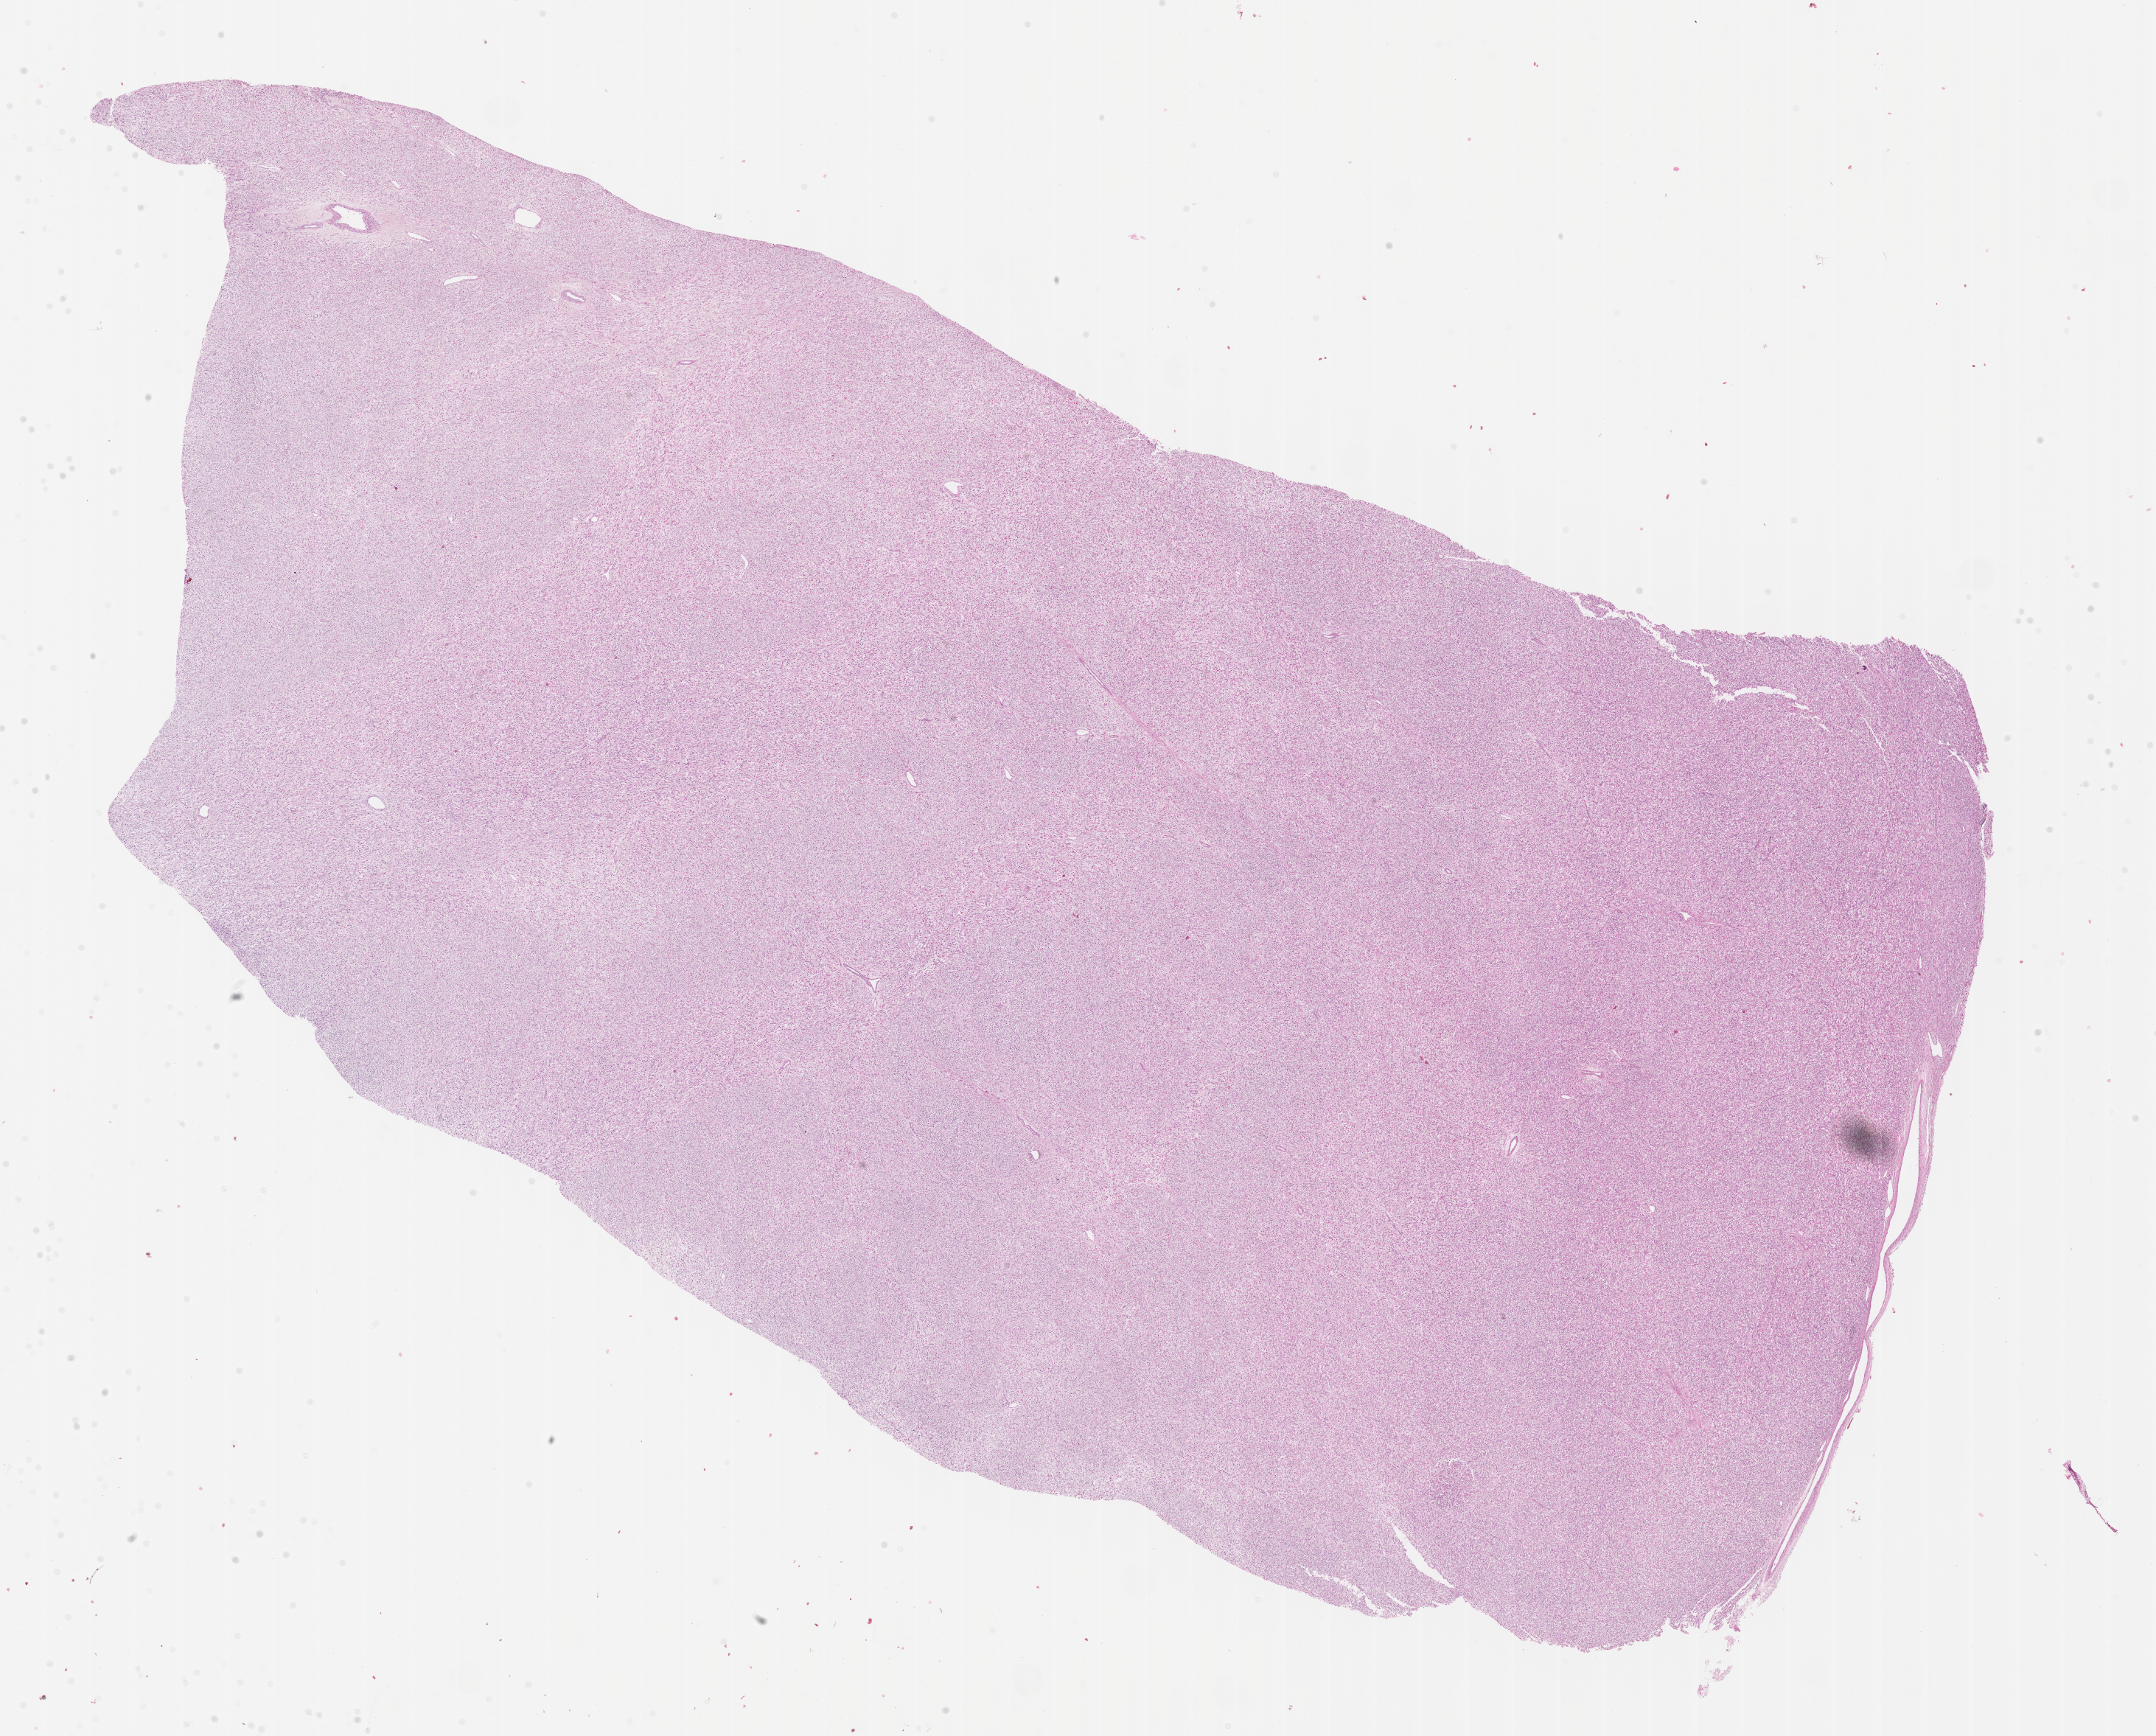
Whole-slide image, H&E stain of tumor tissue — low-resolution overview of the scanned area, about 23.6 x 19.0 mm; formalin-fixed, paraffin-embedded (FFPE) tissue; site: soft tissue - testicle, right. Patient: male, age 19.1 years at diagnosis.
Diagnosis: rhabdomyosarcoma; histological classification: embryonal rhabdomyosarcoma.